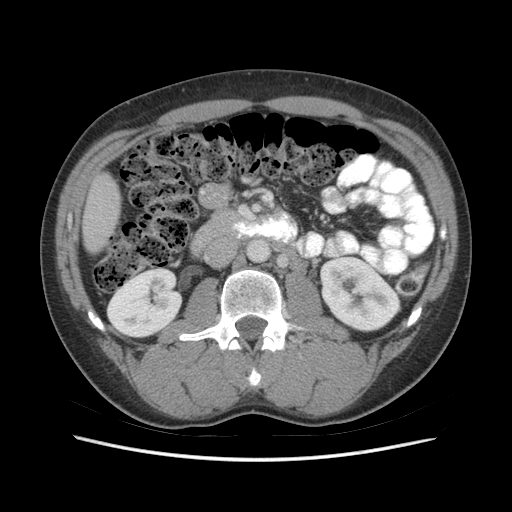
Contrast-enhanced abdominal CT (liver protocol), one axial slice. Slice 12 of 73 in the series (ordered by position). 140 kVp. Soft-tissue window (W 400 / L 40 HU). 2.5 mm slice thickness. 512 × 512 image matrix, field of view 360 × 360 mm. From the clinical record (not read from this slice): diagnosis: hepatocellular carcinoma (patient treated with transarterial chemoembolisation; whether this scan precedes or follows treatment is not stated here); TNM stage (as recorded): Stage-IIIA; Child-Pugh class: A; tumour nodularity: multinodular.
Structures marked on this image (semi-automatically segmented with operator editing):
- liver parenchyma outside the tumour (the mass and vessels are separate outlines, so this box may not span the whole liver): bounding box [x1, y1, x2, y2] px = [82, 173, 120, 252]